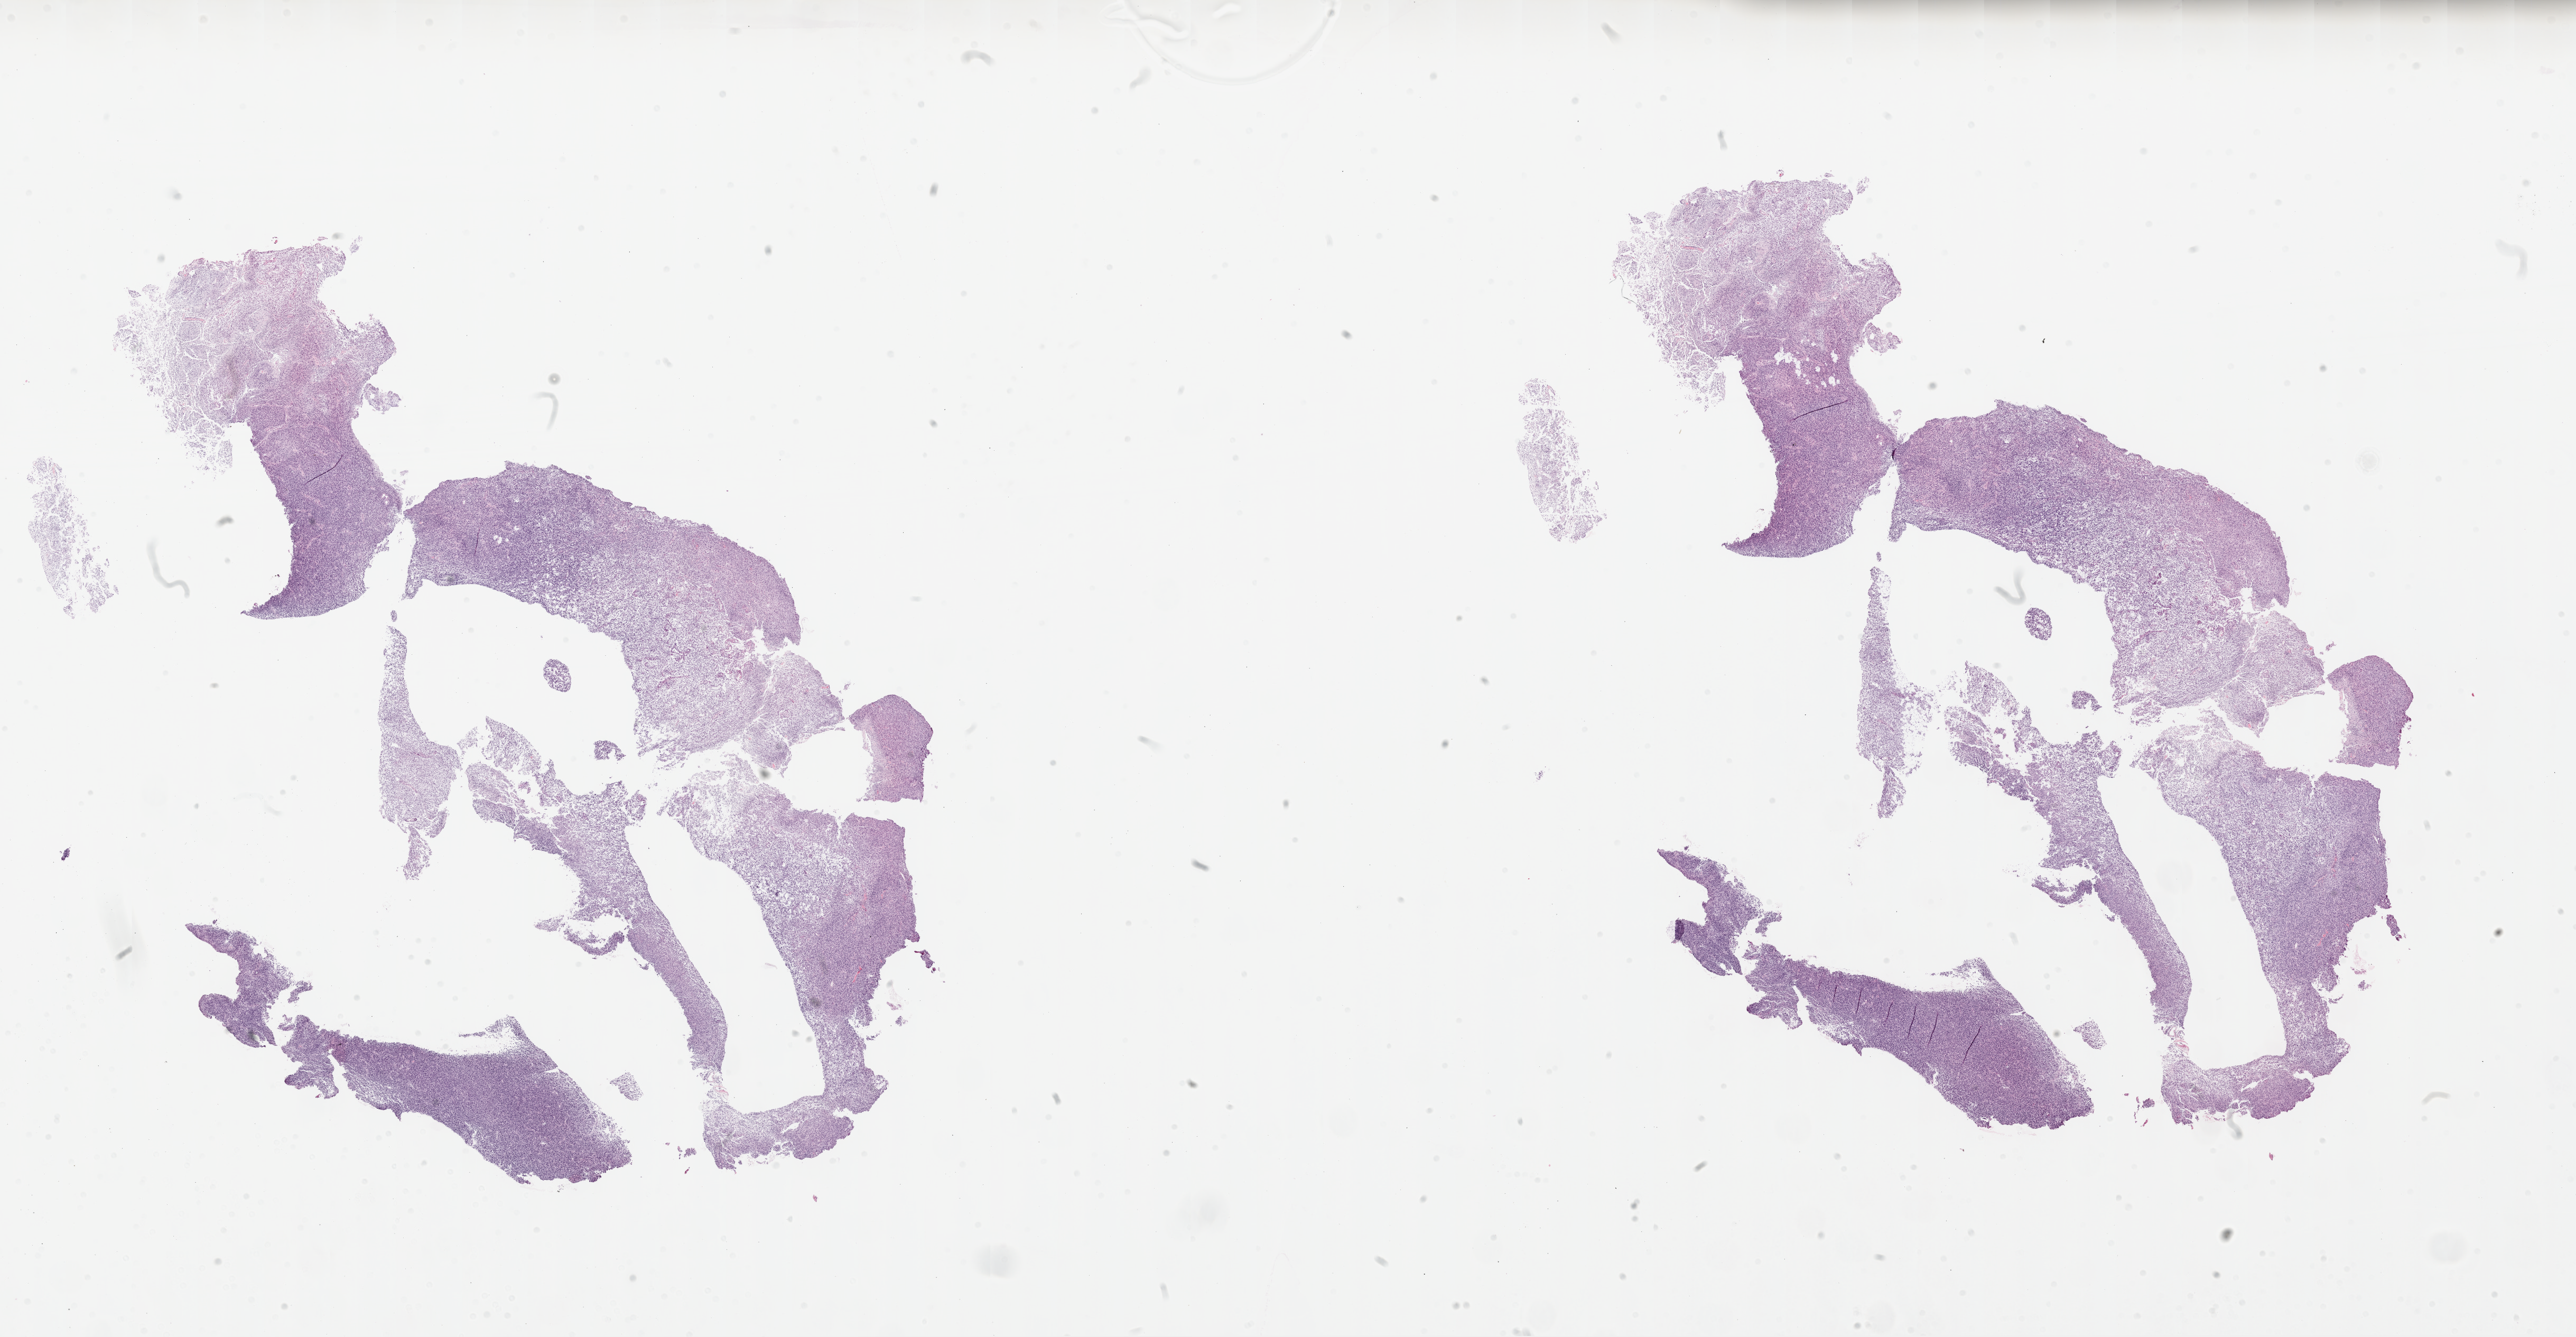
Hematoxylin and eosin (H&E) stained whole-slide image, low-resolution overview of the scanned area, about 39.1 x 20.3 mm (acquisition: 20x scan), FFPE section, brain, primary tumour sample. Male patient; age at initial diagnosis 52 years.
- pathologic diagnosis: Glioblastoma